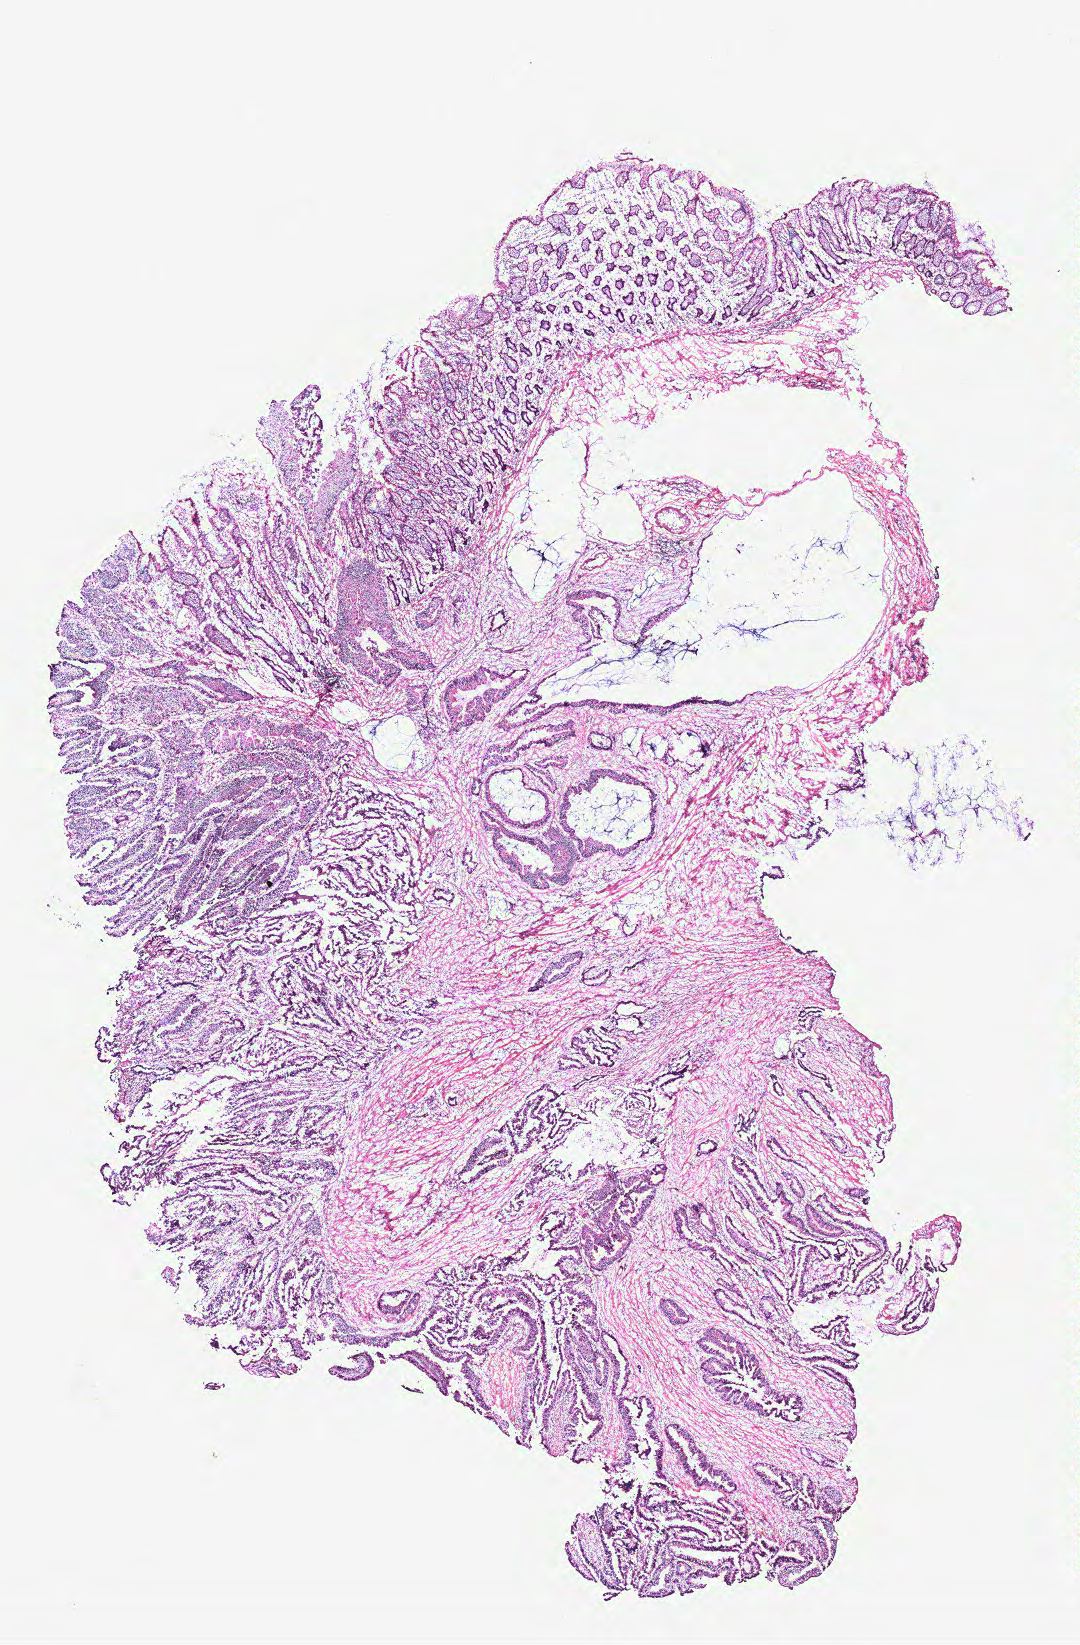
Whole-slide histology image, Hematoxylin and eosin (H&E) stained, low-resolution overview of the scanned area, about 8.6 x 13.2 mm (slide scanned at 40x), colon, tissue type not recorded.
- patient diagnosis (cohort enrolment): colon cancer (colon)